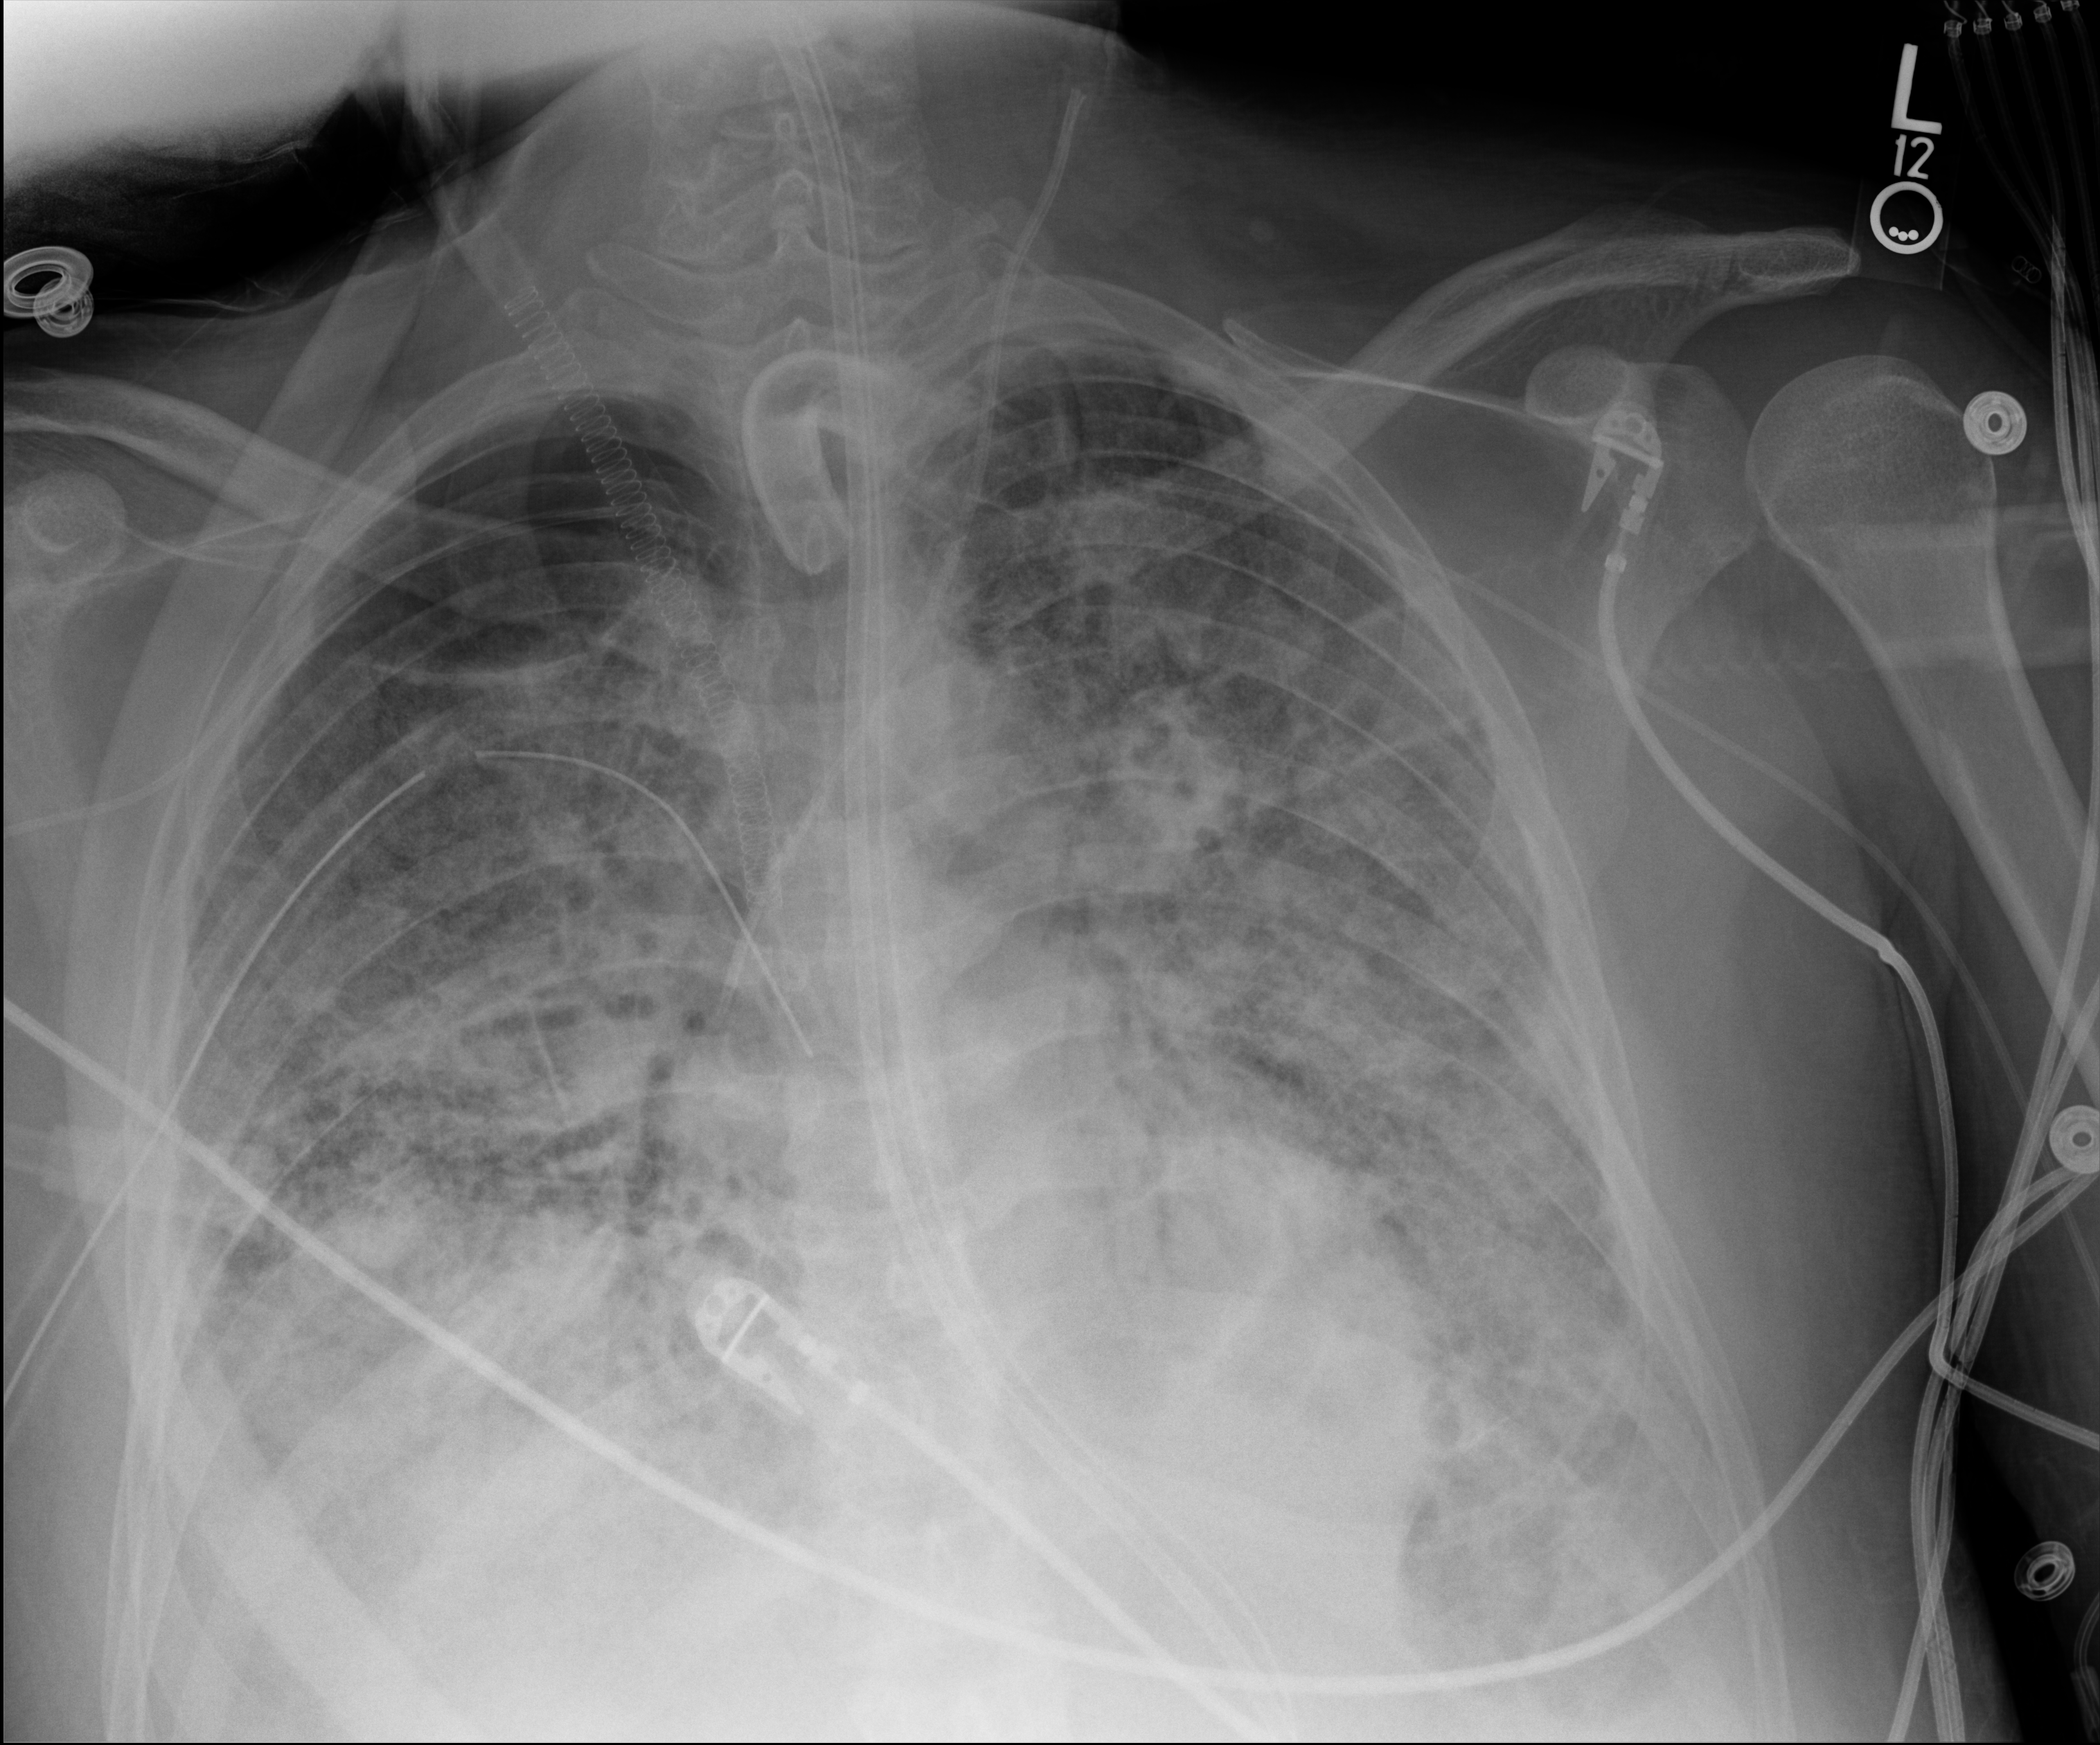
Chest X-ray; anteroposterior (AP) projection. Patient hospitalised with COVID-19, aged 18–59 years.
Hospital-stay facts (about this admission, not read from this image; timing relative to this image not recorded): length of hospital stay: 60 days.